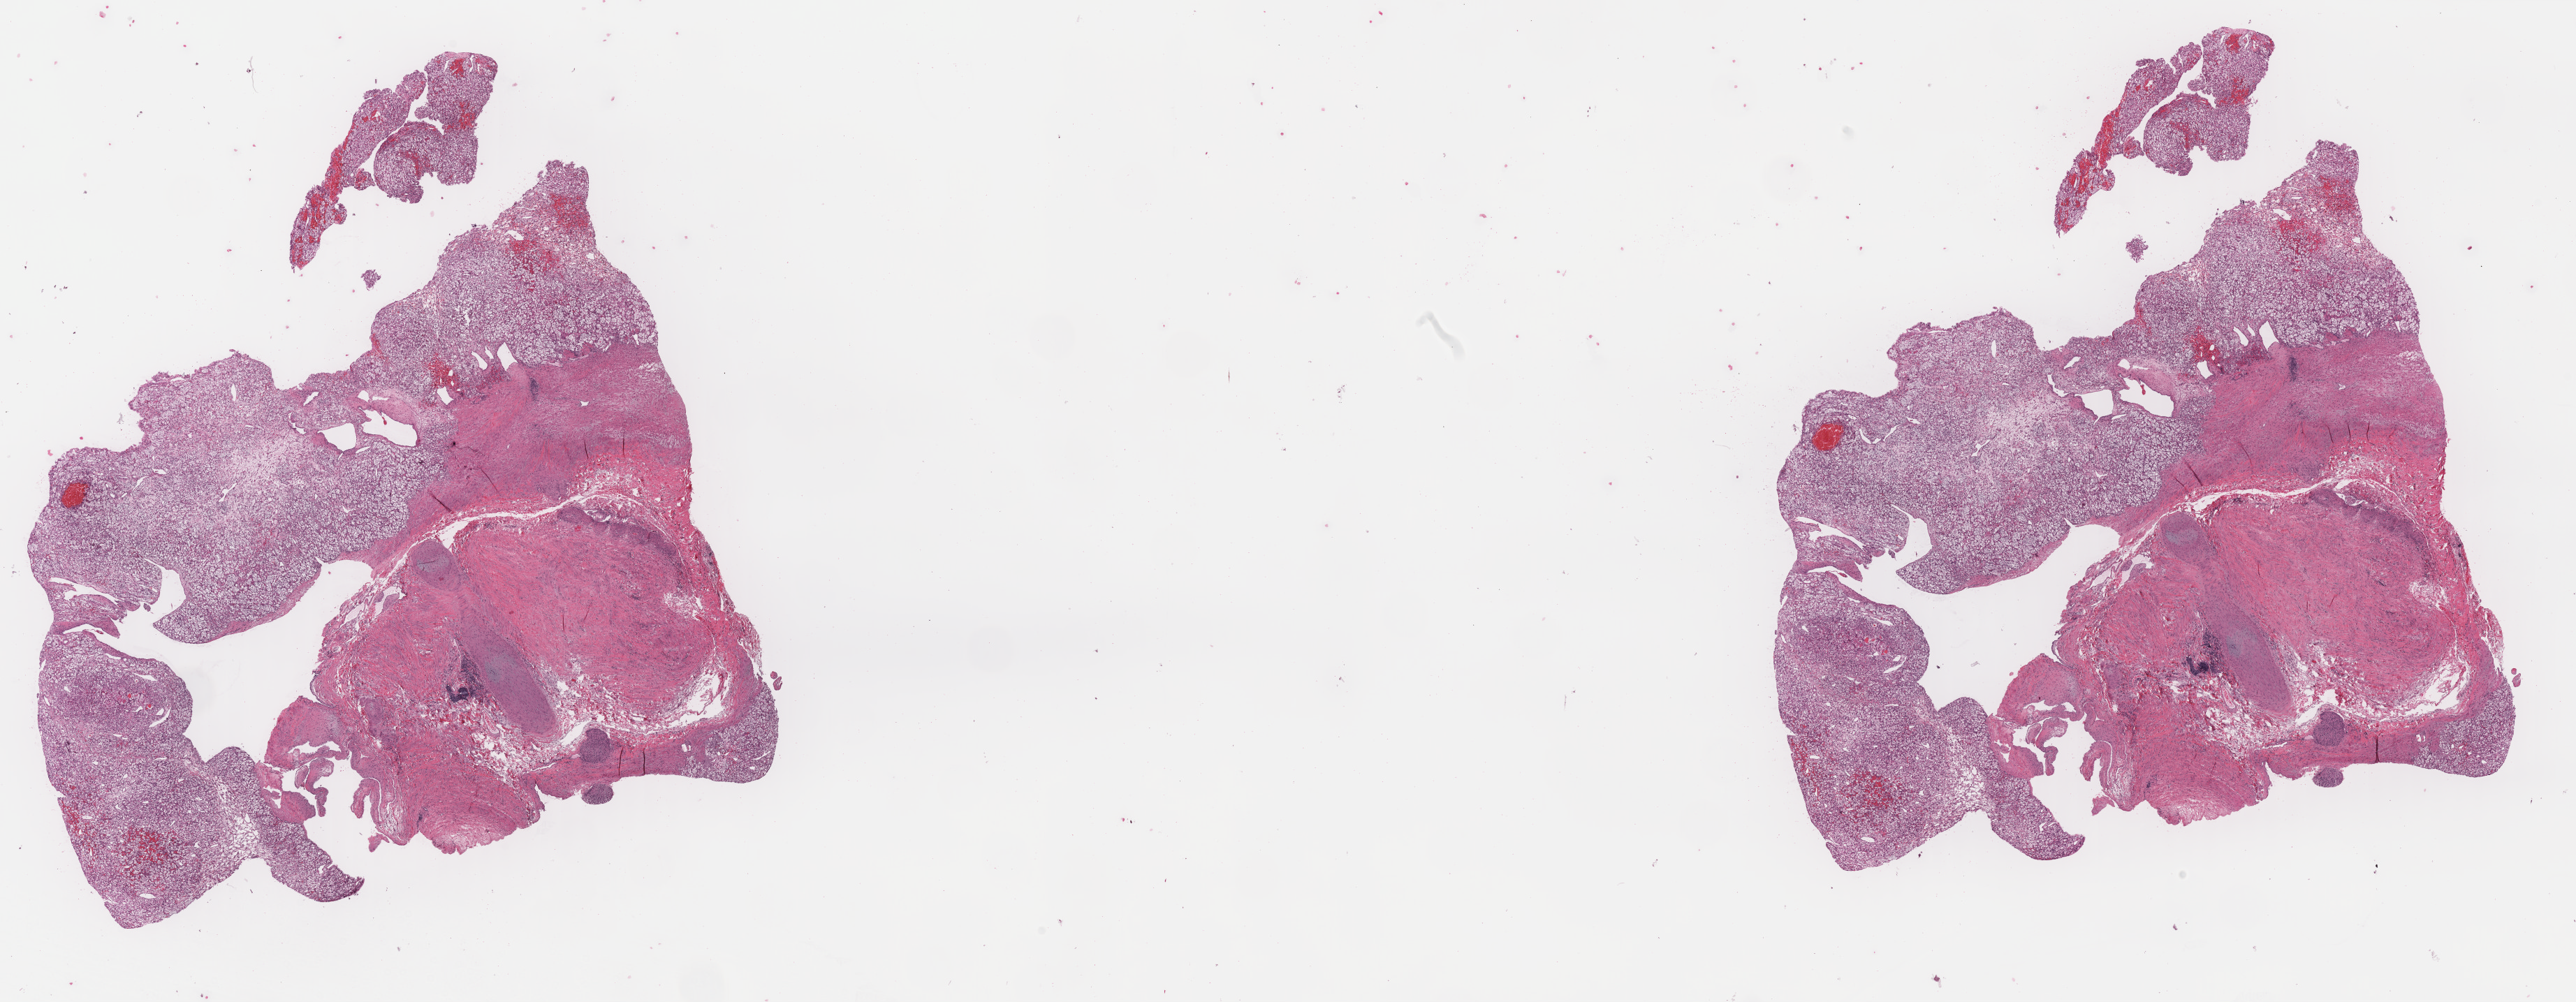
Digitized H&E tissue section (whole slide), shown as a low-resolution overview of the whole scanned area (about 29.2 x 11.4 mm, from a 40x scan). Formalin-fixed paraffin-embedded (FFPE) diagnostic section. Primary tumour sample from the kidney. Male patient; age at initial diagnosis 60 years. Histologic grade: G2 (moderately differentiated).
Laterality: right. Diagnosis: Renal cell carcinoma, NOS. AJCC pathologic stage: II. TNM: T2a NX MX.